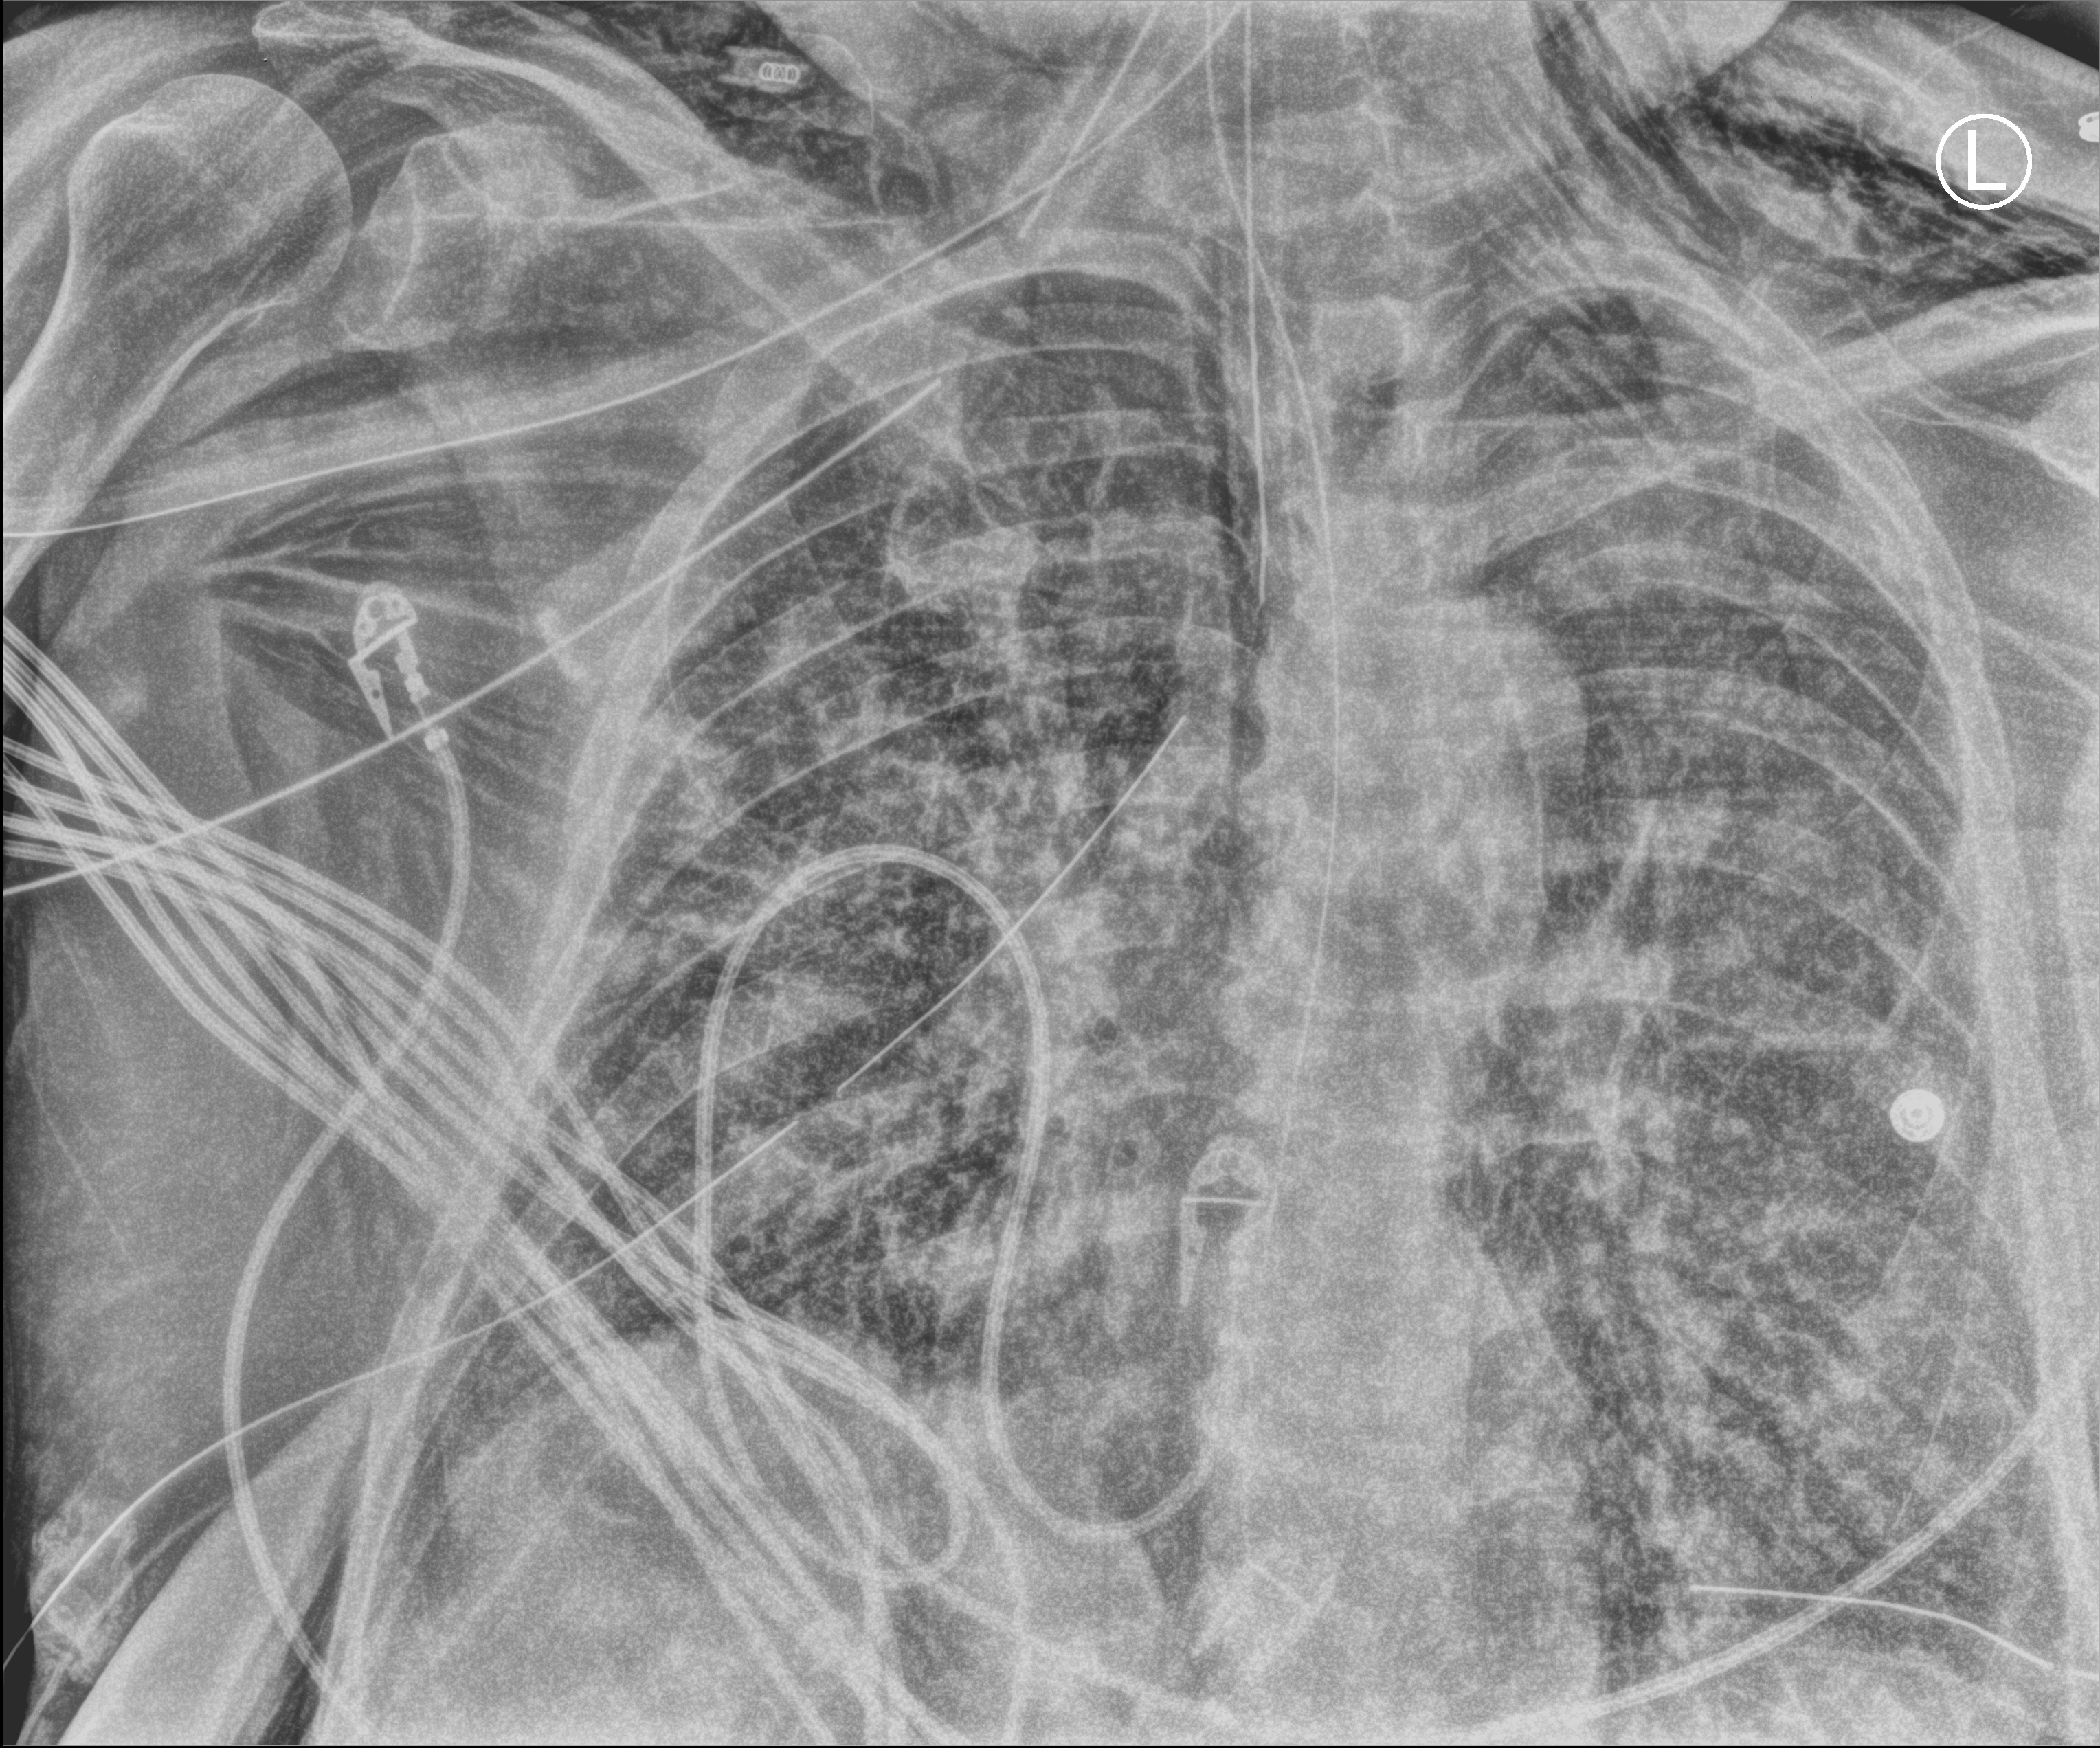
Bedside chest radiograph (computed radiography), anteroposterior (AP) projection. Adult patient hospitalised with COVID-19, age 18–59 years.
From the hospital-stay record, not from the radiograph (when in the stay this image was taken is not recorded): mechanically ventilated during this hospital stay: yes; length of hospital stay: 28 days; admitted to intensive care during this hospital stay: yes.